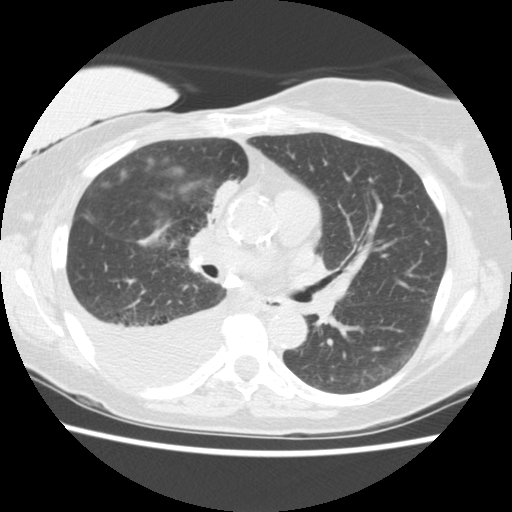
Low-dose screening chest CT, axial slice; third screening round (two years after baseline); lung window (W 1500 / L -600 HU); standard (soft-tissue) reconstruction kernel (STANDARD); 120 kVp; slice 74 of 157 in the series. Female, age 56 years at enrolment. Current smoker at enrolment.
- Expert-annotated lung lesion, bounding box <185,166,251,234> (left, top, right, bottom; pixels).
- The screening reader recorded 2 non-calcified nodules or masses ≥4 mm on this exam (right middle lobe, right lower lobe); which of them this box marks is not recorded.
- Later outcome: lung cancer diagnosed 160 days after this screen — adenocarcinoma, NOS, right upper lobe, stage IIIB (AJCC 6th edition), 8 mm at pathology.